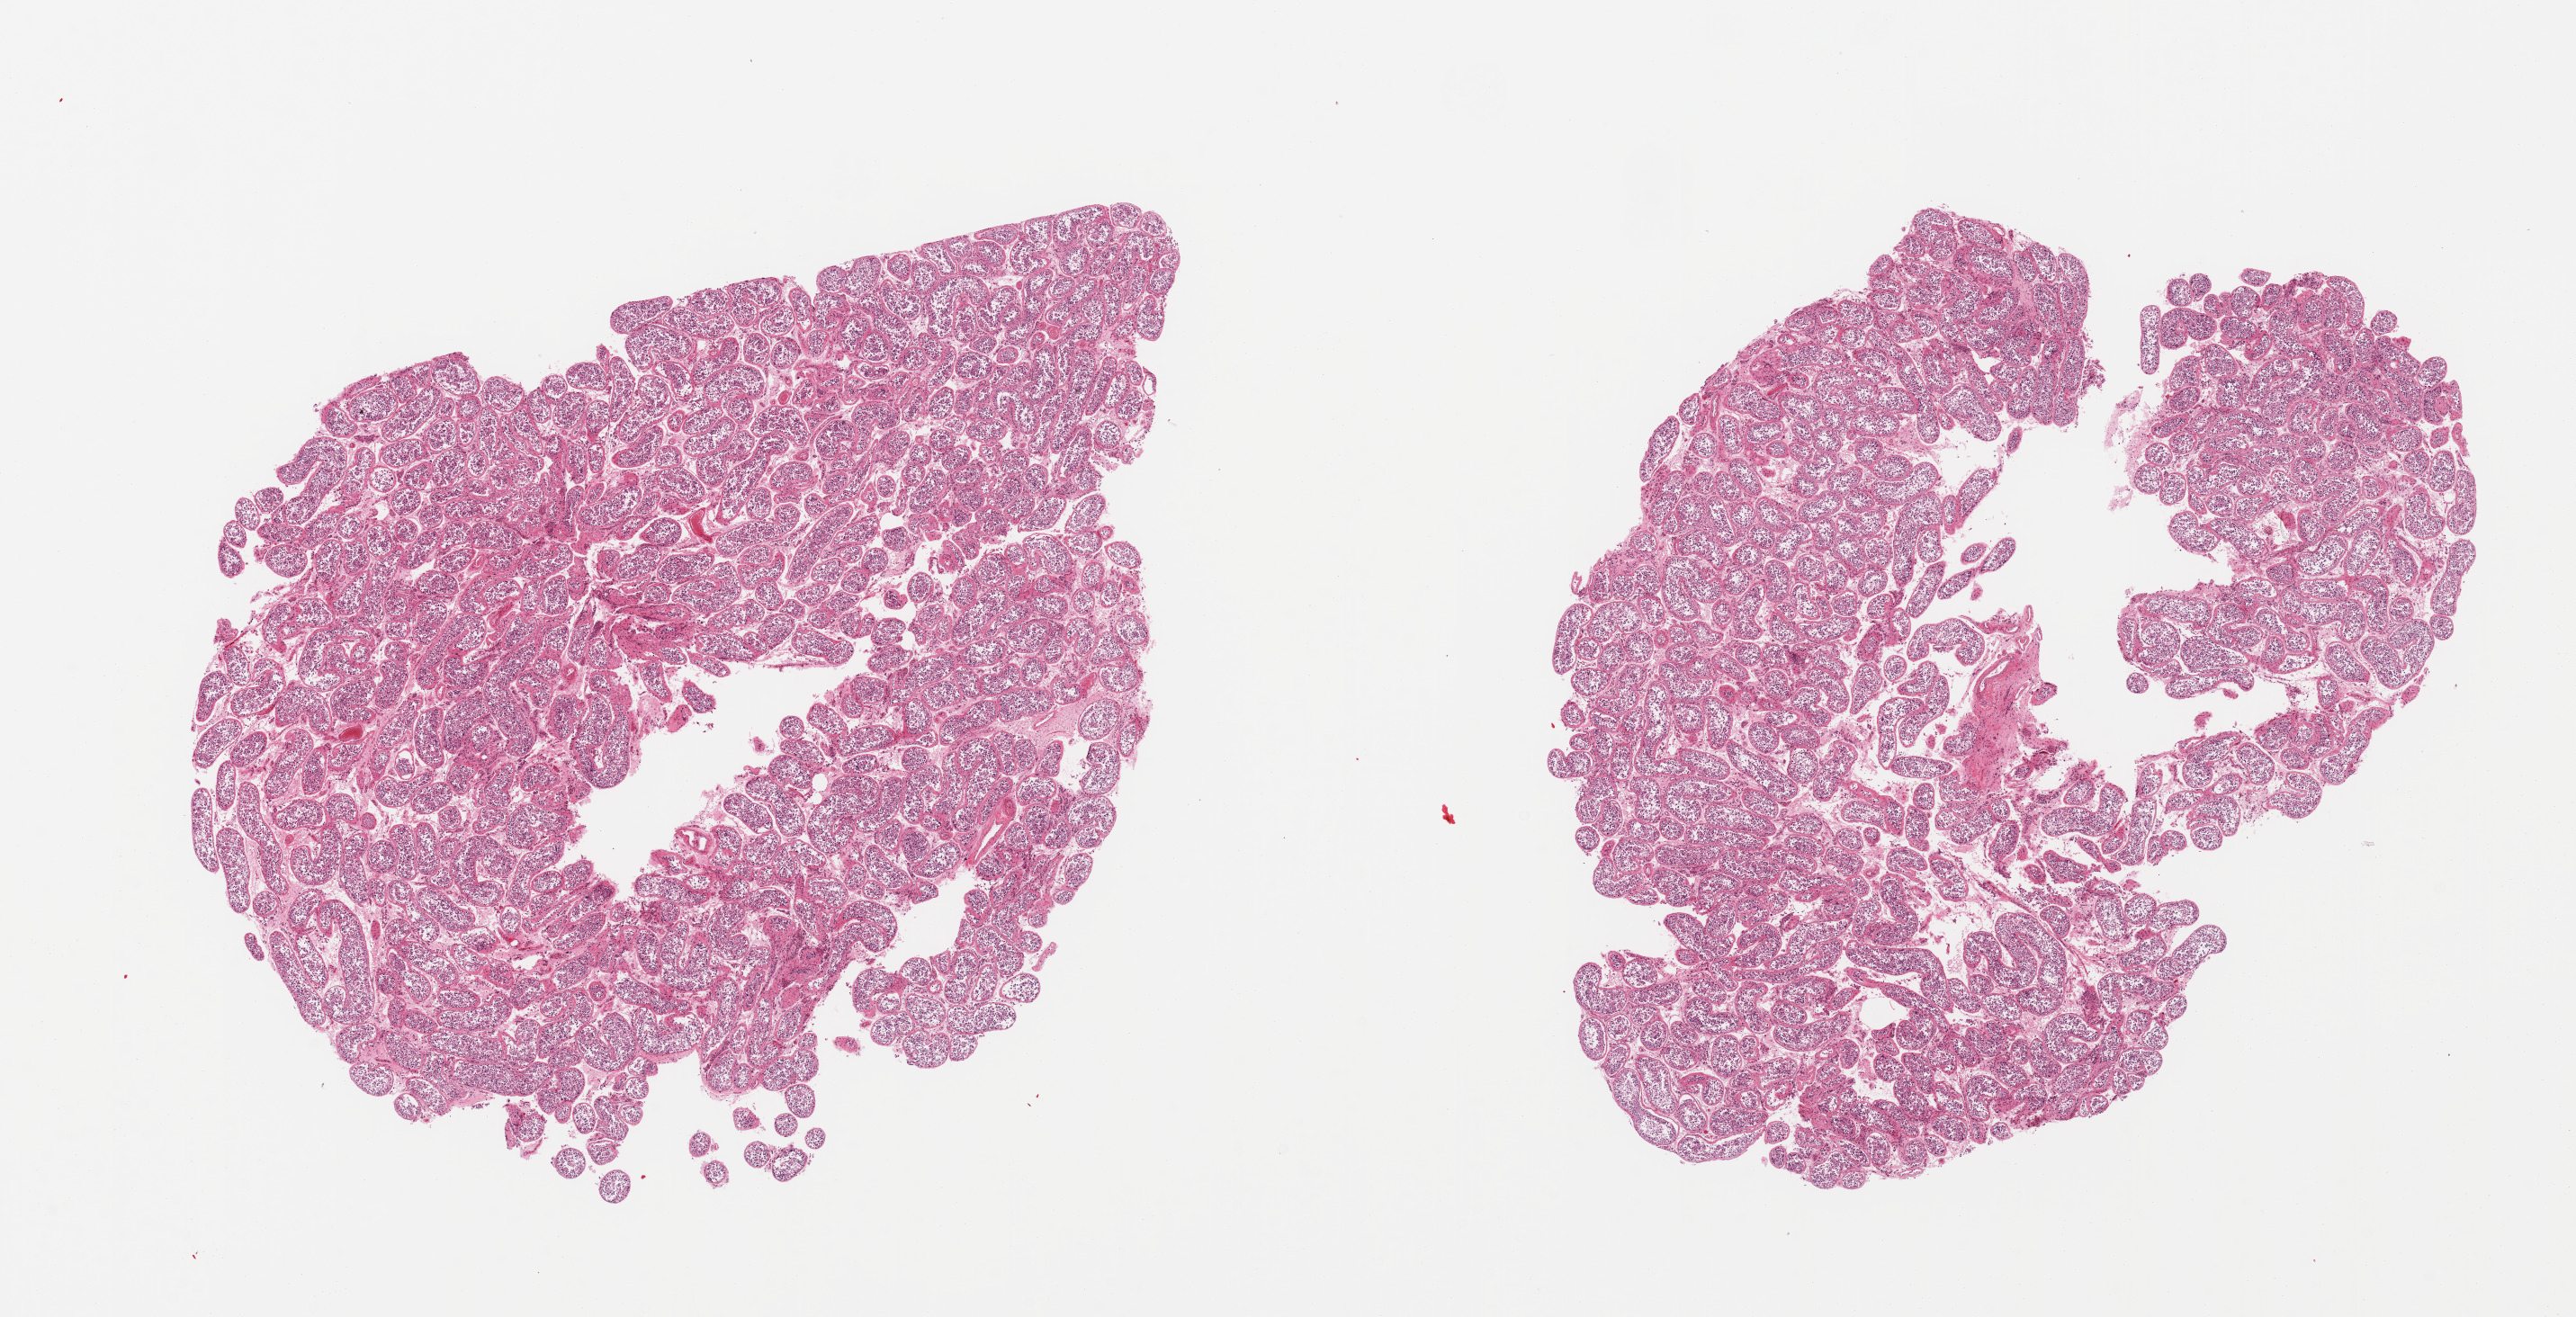
Digitized hematoxylin and eosin (H&E)-stained section, a low-resolution overview of the entire scanned area, about 22.6 x 11.6 mm (from a 20x scan), PAXgene-fixed paraffin-embedded (PFPE) section, target tissue: testis, tissue donor sample.
Reviewer comment on this tissue sample: 2 pieces; spermatogenesis.